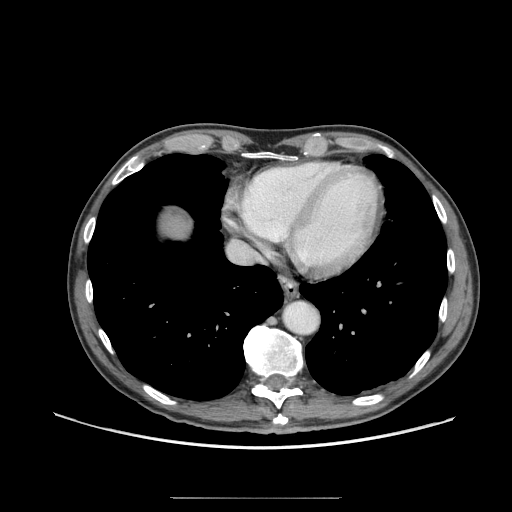
Contrast-enhanced abdominal CT (liver protocol), one axial slice. Slice 67 of 71 in the series (ordered by position). 140 kVp. Soft-tissue window (W 400 / L 40 HU). 512 × 512 image matrix, field of view 400 × 400 mm. From the clinical record (not read from this slice): diagnosis: hepatocellular carcinoma (patient treated with transarterial chemoembolisation; whether this scan precedes or follows treatment is not stated here); TNM stage (as recorded): Stage-I; Child-Pugh class: A; tumour differentiation: well differentiated; tumour nodularity: uninodular.
Outlined on this slice (semi-automatic segmentation, software-assisted and operator-edited):
- abdominal aorta: bounding box [x1, y1, x2, y2] px = [283, 302, 318, 334]
- liver parenchyma outside the tumour (the mass and vessels are separate outlines, so this box may not span the whole liver): [162, 214, 188, 236]